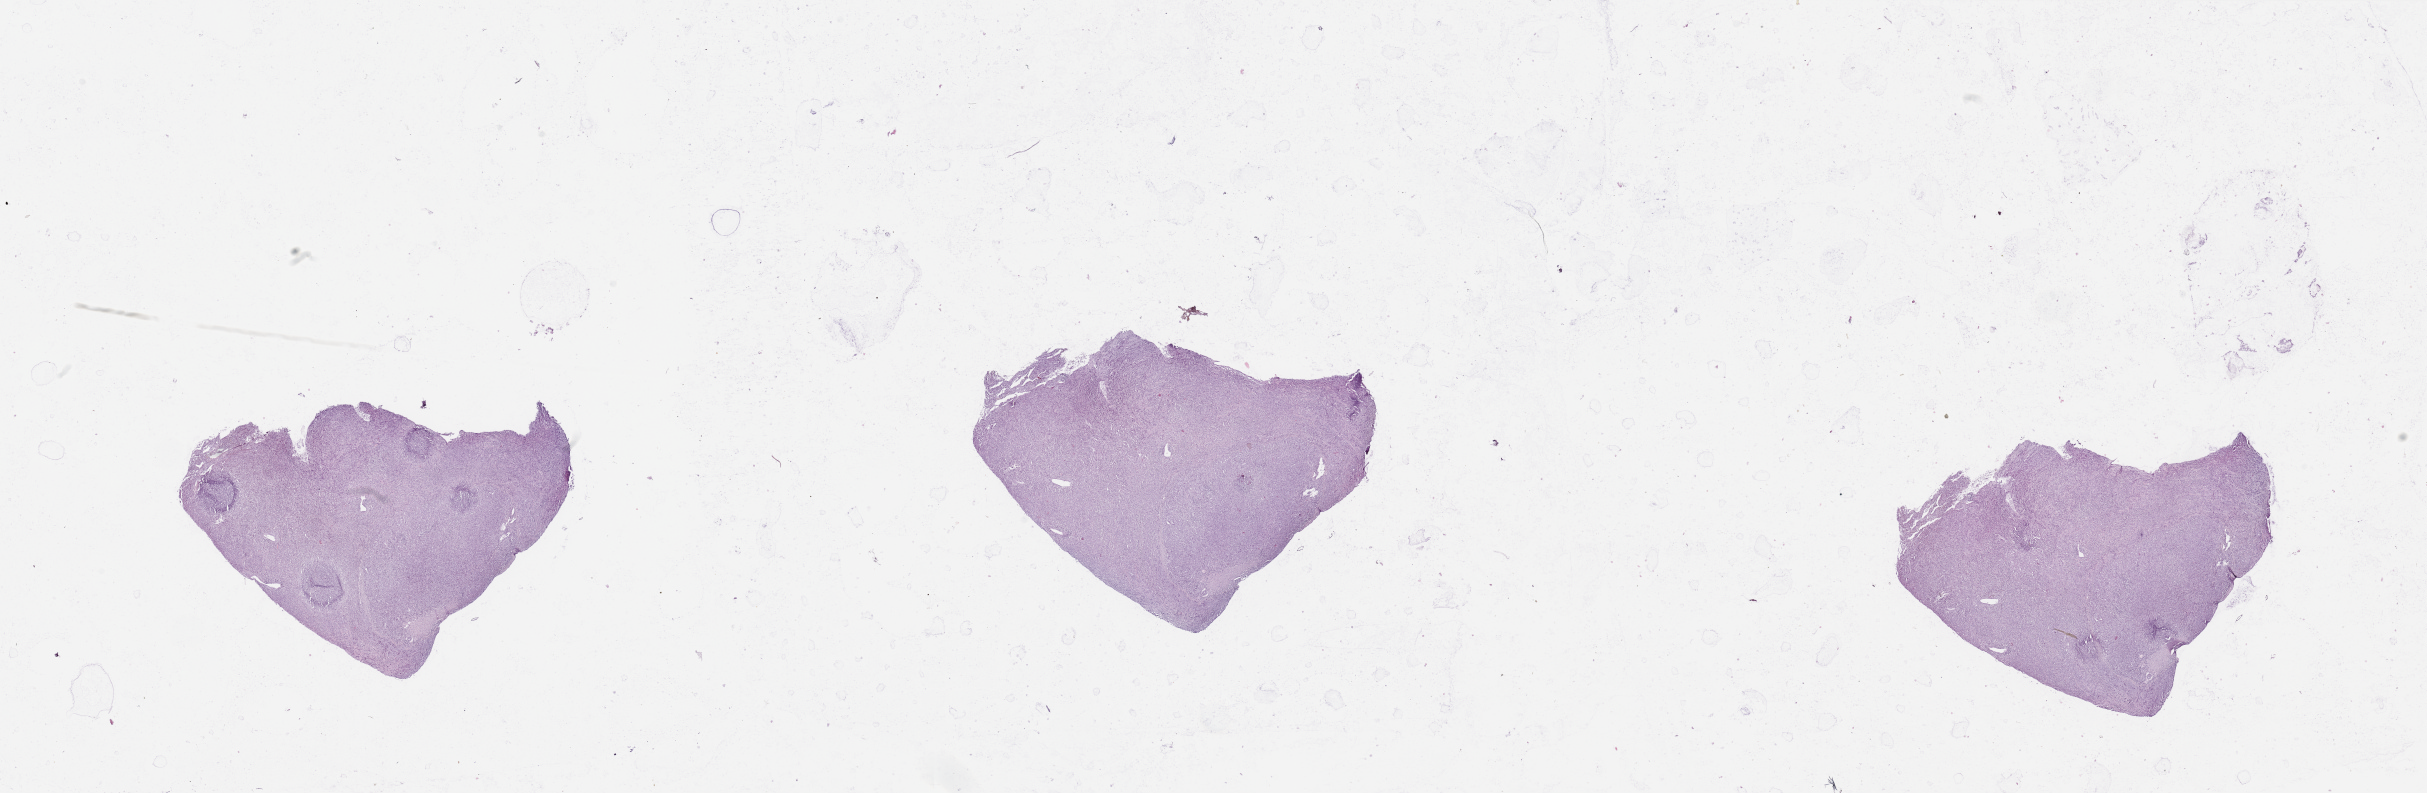
Digitized H&E tissue section (whole slide) — whole scanned area (about 38.4 x 12.5 mm) shown as a low-resolution overview. Tumour tissue sample, sampled site: lung. 51-year-old male patient. Composition of this section per pathologist review: tumour nuclei 80%, necrosis 3%.
Diagnosis: Squamous cell carcinoma, NOS.